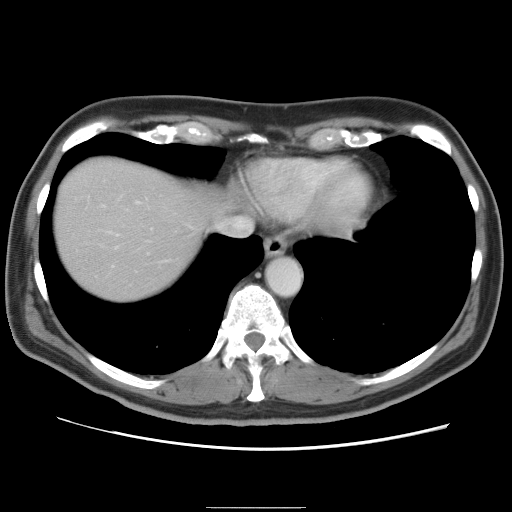
Contrast-enhanced abdominal CT, one axial slice; position 74 of 87 along the scan axis; 120 kVp; intravenous contrast given; soft-tissue window (W 400 / L 40 HU); 512 × 512 image matrix. Male patient, age 63 years. From the clinical record (not read from this slice): diagnosis: colorectal cancer liver metastases, imaged before liver resection; multiple liver metastases: no; largest metastasis: 9 cm.
Outlined on this slice (outlined manually by an expert reader):
- hepatic veins: bounding box (x1, y1, x2, y2) in pixels: (105, 198, 250, 242)
- liver: (52, 157, 212, 305)
- planned liver remnant (the part of the liver to remain after resection): (53, 174, 201, 303)
- portal vein (with intrahepatic branches): (97, 193, 154, 268)